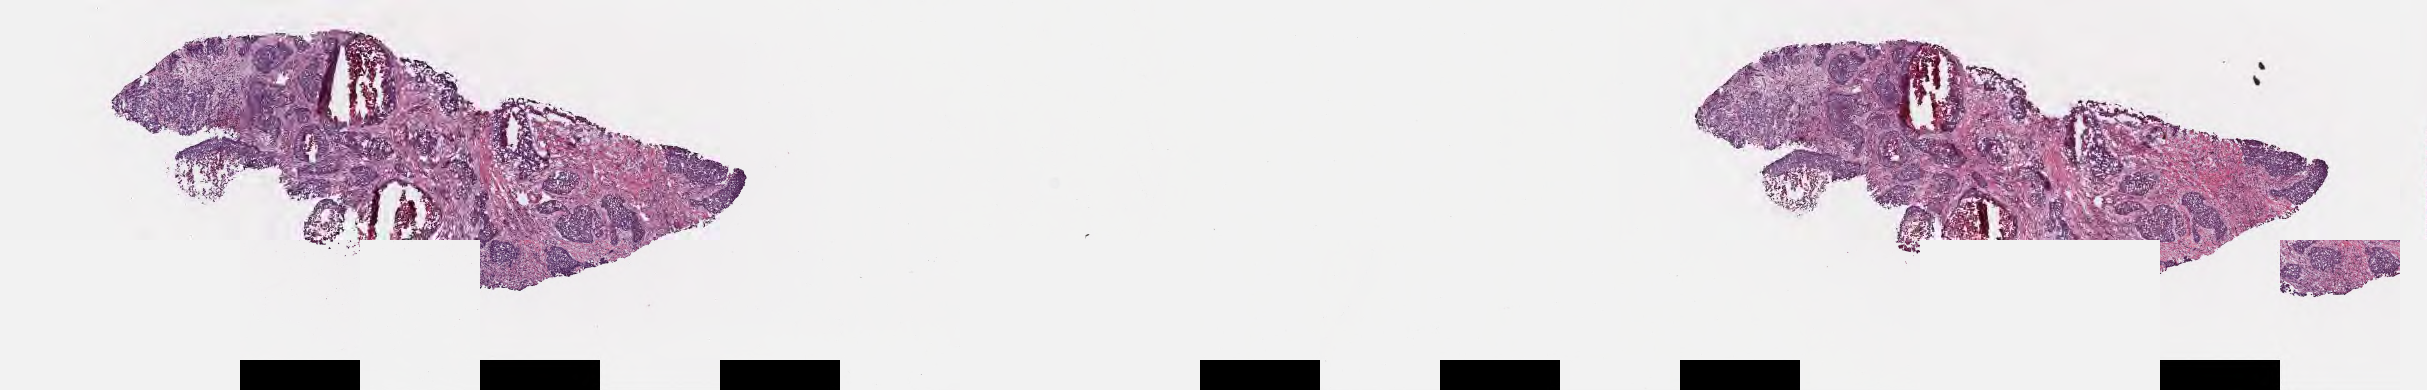
Whole-slide image, haematoxylin and eosin stain — low-resolution overview of the scanned area, about 19.6 x 3.2 mm, frozen section (tissue freezing medium), specimen: primary tumor, site: lower lobe of left lung. Patient: male, age 66 years. Pathologist review of this section (percent, as recorded): tumor cells 85%, tumor nuclei 65%, stromal cells 0%, necrosis 15%, normal cells 0%. Inflammatory infiltration, as recorded: lymphocyte infiltration 0%, monocyte infiltration 0%, neutrophil infiltration 0%.
Diagnosis: Adenocarcinoma with mixed subtypes. AJCC pathologic stage: Stage IA.